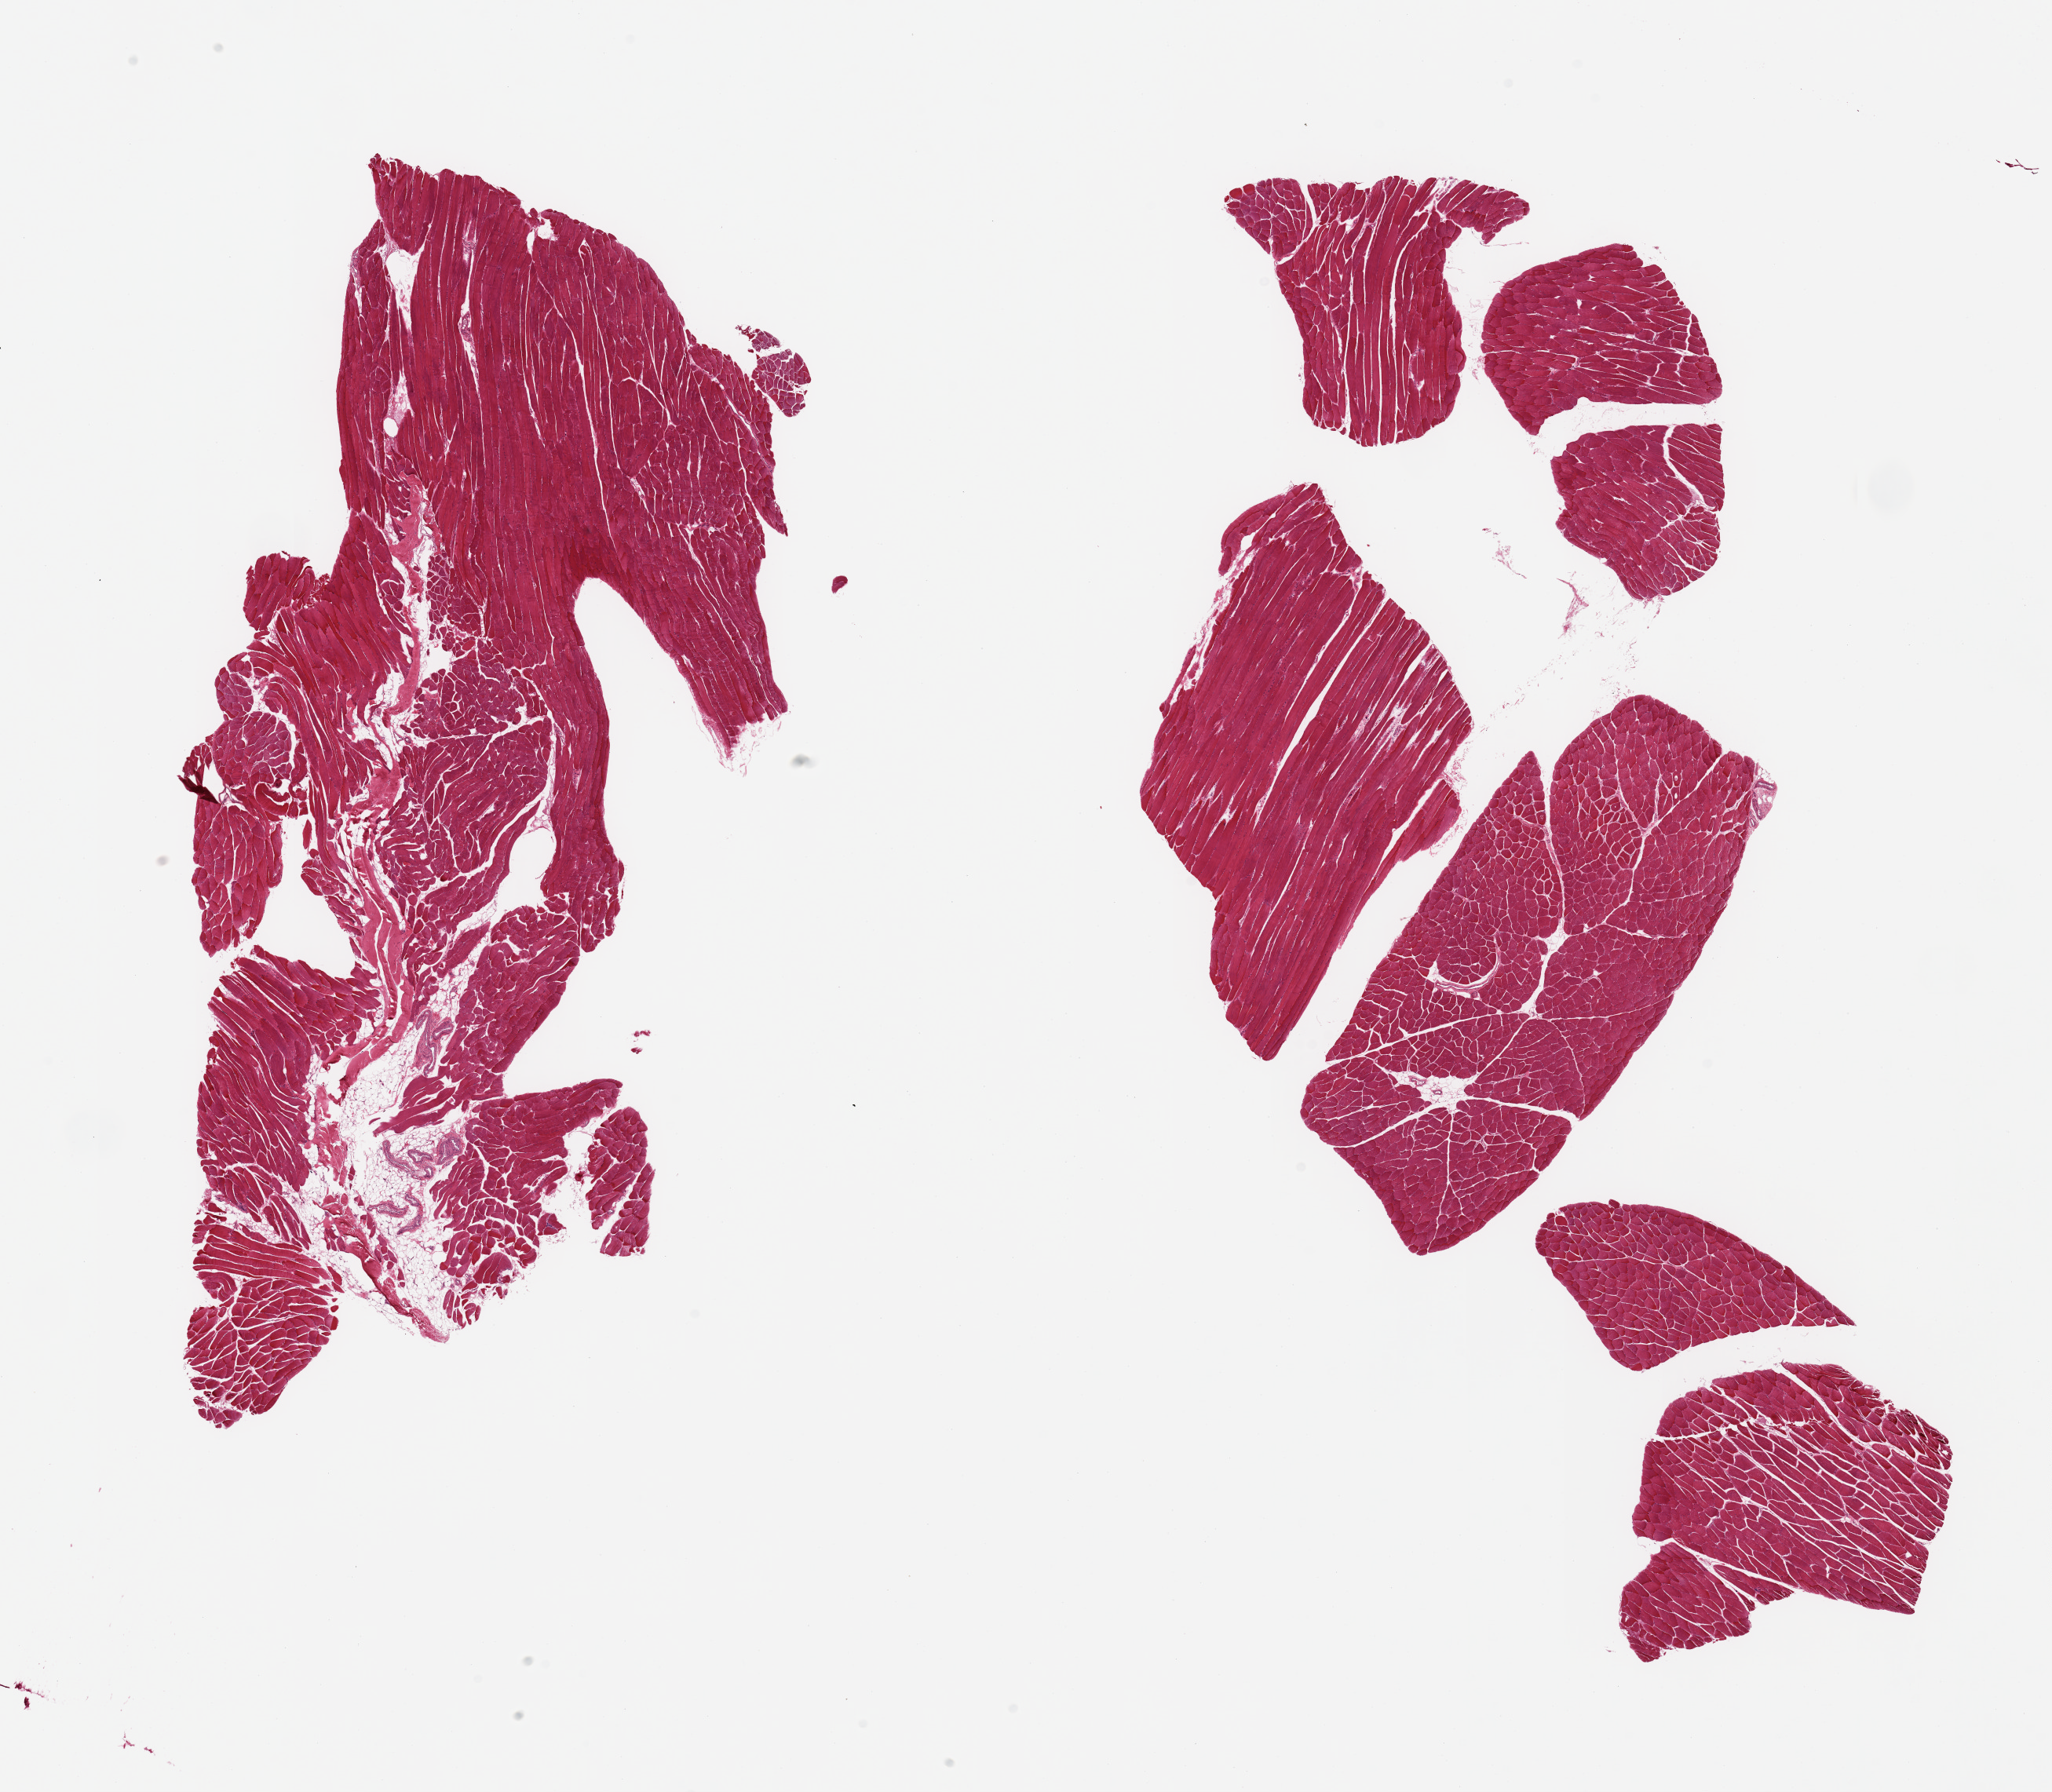
Hematoxylin and eosin (H&E) whole-slide image, whole scanned area (about 20.7 x 18.1 mm, from a 20x scan) shown as a low-resolution overview. PAXgene-fixed paraffin-embedded (PFPE) section. Sampled site (target tissue): skeletal muscle. Tissue donor sample.
Pathologist's review note for this sample: 2 pieces; fragmented; 1 with 5% internal fat.